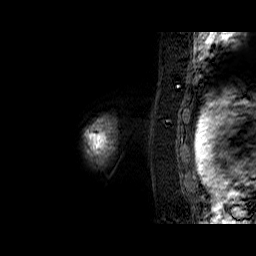
Breast MRI (dynamic contrast-enhanced), one sagittal slice. Position 57 of 60 along the scan axis. Dynamic contrast-enhanced series, time point 2 of 6 at this slice position (early post-contrast). 1.5 T. TE 6.3 ms, TR 32.9 ms. 256 × 256 image matrix, field of view 200 × 200 mm. Female patient. From the clinical record (not read from this slice): setting: breast cancer imaged before/during neoadjuvant chemotherapy; receptor status: triple-negative.
Structures marked on this image (semi-automatically segmented with operator editing):
- analysis volume of interest (the breast-tissue region the enhancement analysis was run in; not a lesion): bounding box (x1, y1, x2, y2) in pixels: (85, 115, 117, 165)
- tumour enhancement mask (voxels above the 100 % enhancement threshold inside the analysis volume of interest): (85, 119, 112, 155)